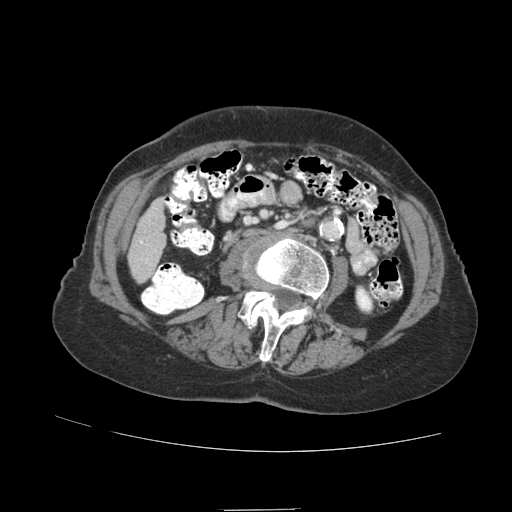
Contrast-enhanced abdominal CT (liver protocol), one axial slice. Slice 14 of 89 in the series (ordered by position). Reconstruction kernel STANDARD. 140 kVp. Soft-tissue window (W 400 / L 40 HU). 2.5 mm slice thickness. 512 × 512 image matrix. Case-level facts recorded for this patient, not image findings: diagnosis: hepatocellular carcinoma (patient treated with transarterial chemoembolisation; whether this scan precedes or follows treatment is not stated here); TNM stage (as recorded): Stage-II; Child-Pugh class: A; tumour size: 4 cm.
Structures marked on this image (semi-automatically segmented with operator editing):
- liver parenchyma outside the tumour (the mass and vessels are separate outlines, so this box may not span the whole liver): bounding box (x1, y1, x2, y2) in pixels: (128, 198, 166, 282)
- liver vessels: (140, 240, 148, 261)